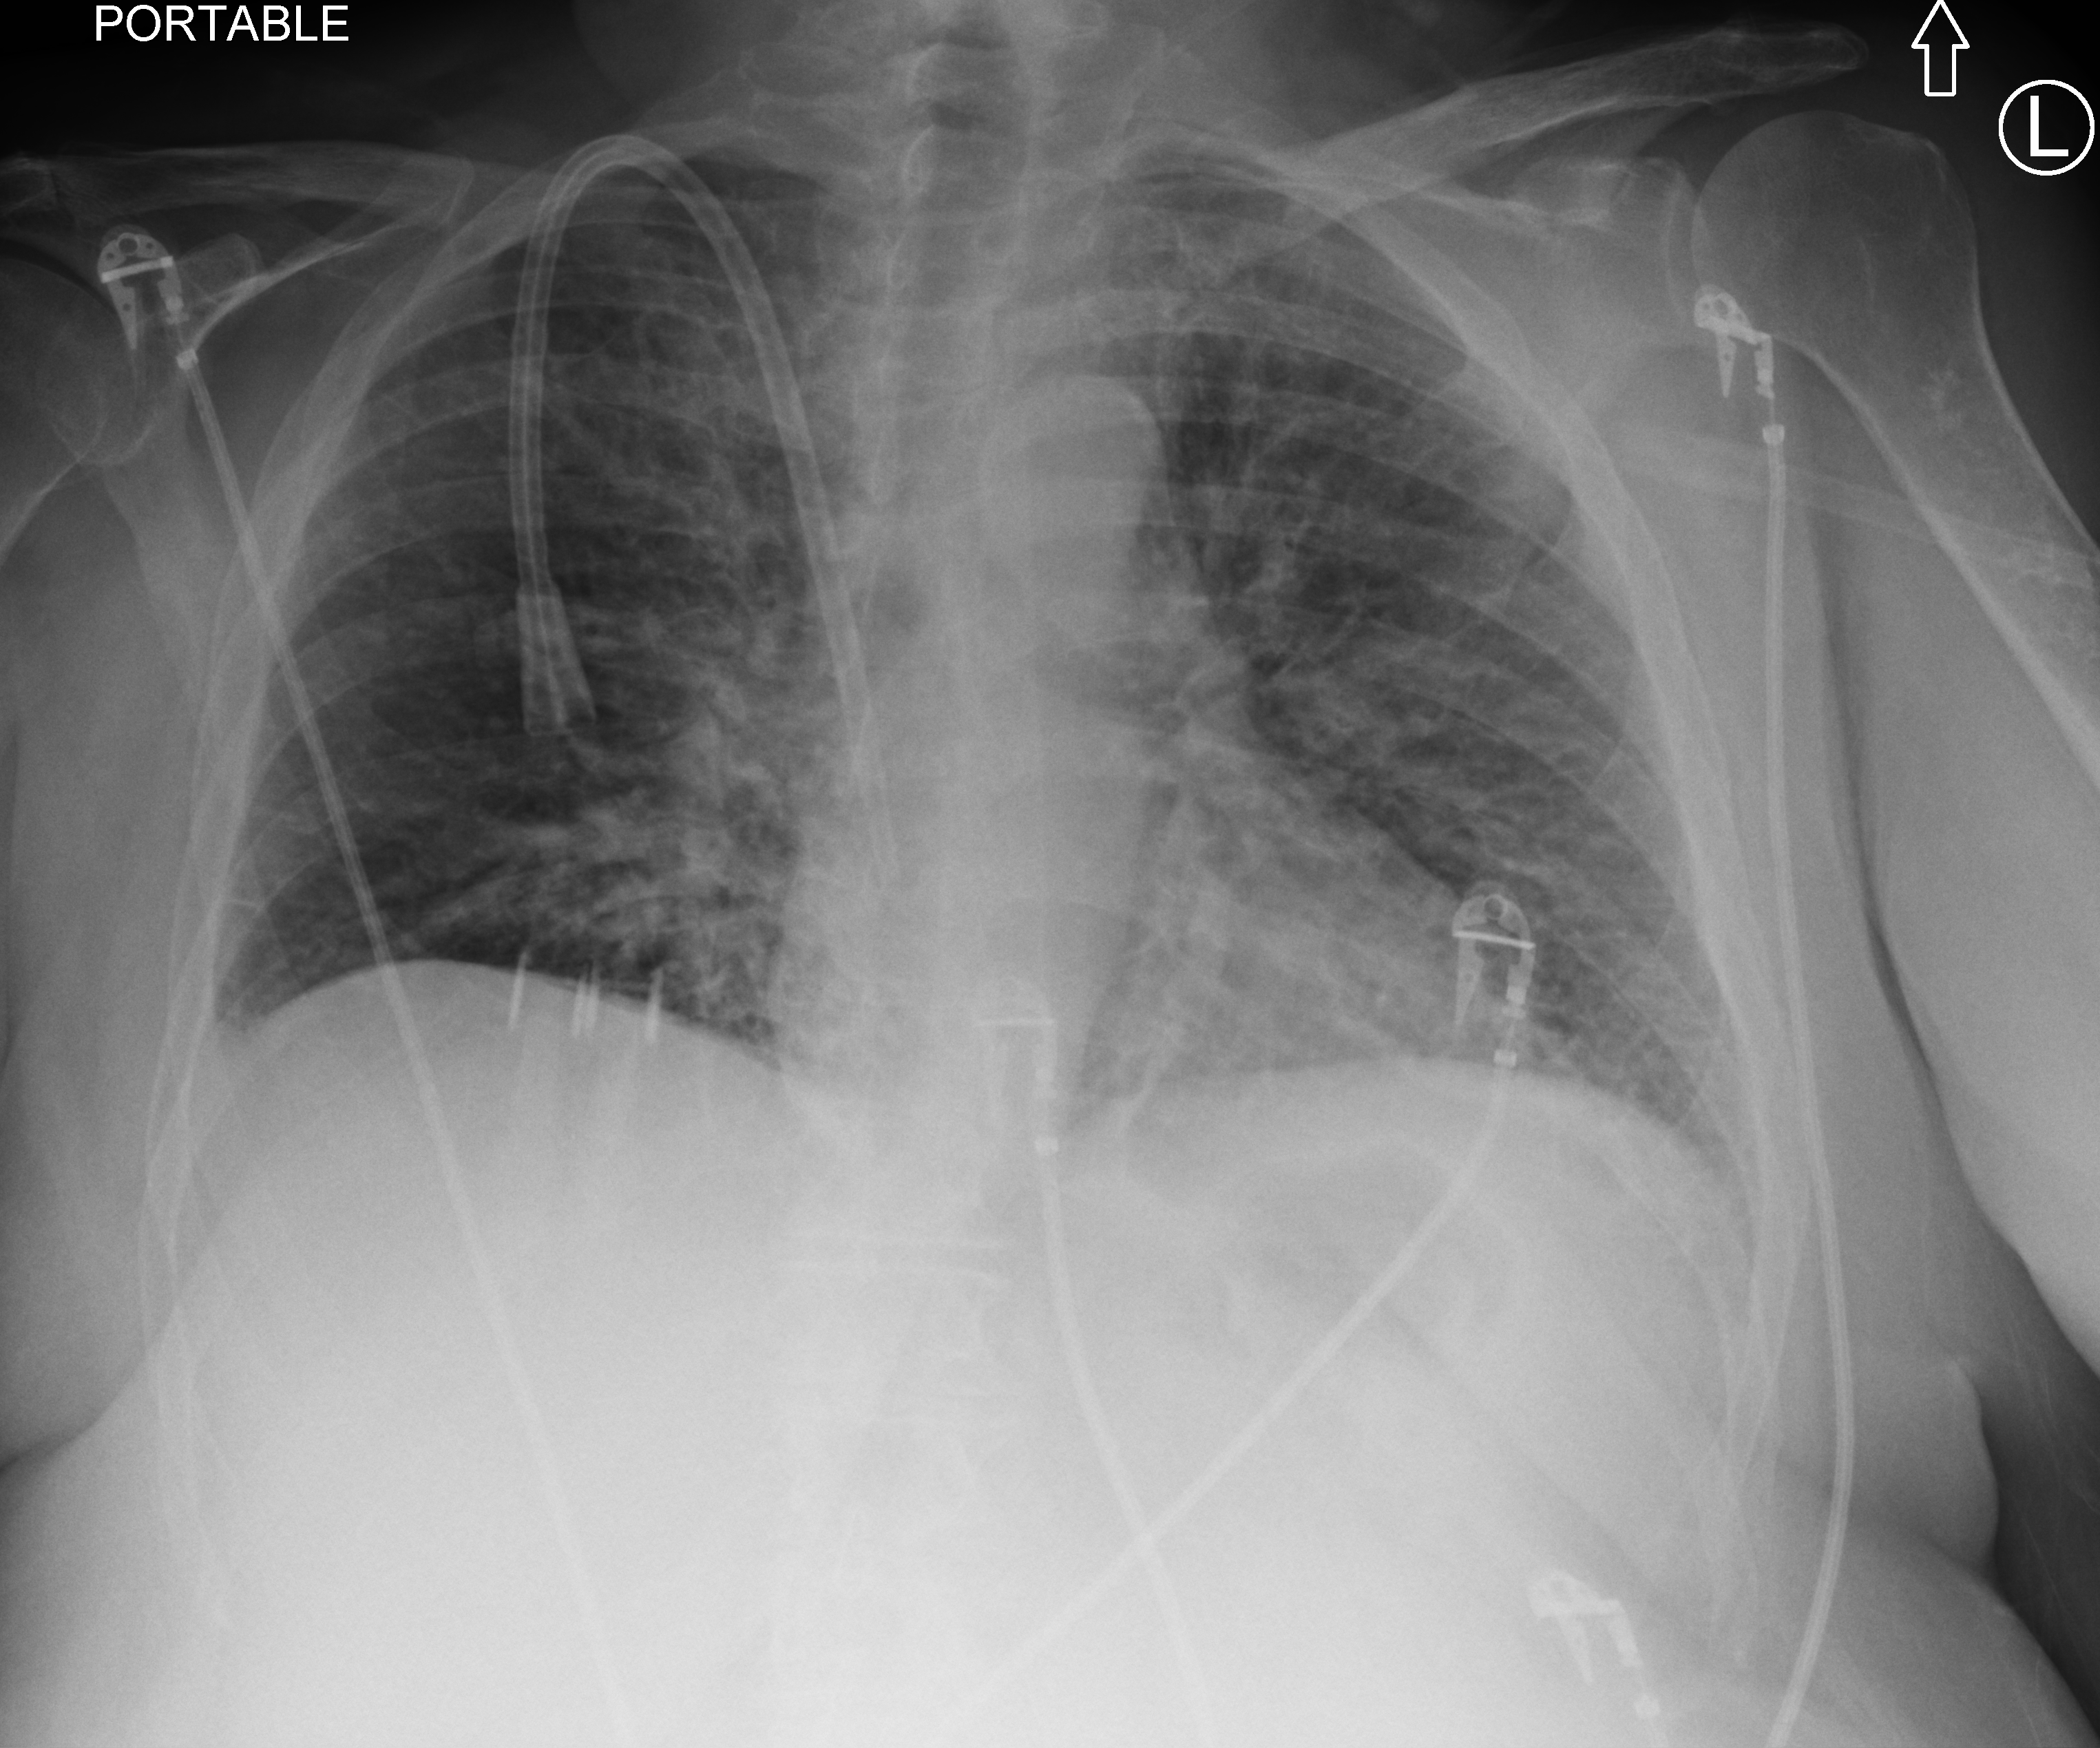
Bedside chest radiograph (computed radiography). Patient hospitalised with COVID-19; female, aged 60–74 years.
Hospital-stay facts (about this admission, not read from this image; timing relative to this image not recorded):
- mechanically ventilated during this hospital stay: no